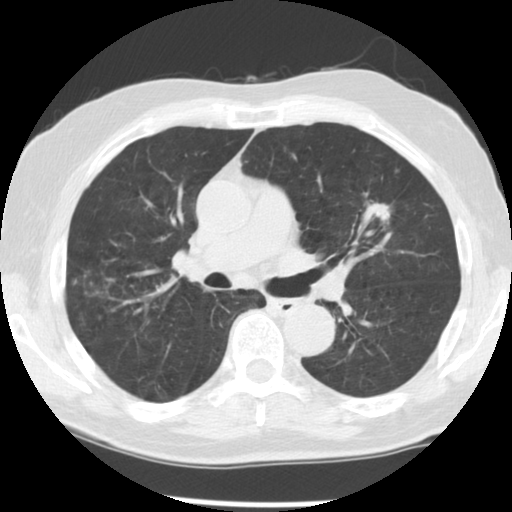
Axial slice from a low-dose chest CT screening exam, third screening round (two years after baseline), lung window (W 1500 / L -600 HU), standard (soft-tissue) reconstruction kernel (STANDARD), 140 kVp, slice 76 of 131 in the series, 512 × 512 image matrix, field of view 330 × 330 mm. Male participant, aged 70 years at enrolment. Current smoker at enrolment.
- Lesion marked by an expert reader, bounding box <356,185,411,241> (left, top, right, bottom; pixels).
- The screening reader recorded 3 non-calcified nodules or masses ≥4 mm on this exam; which of them this box marks is not recorded.